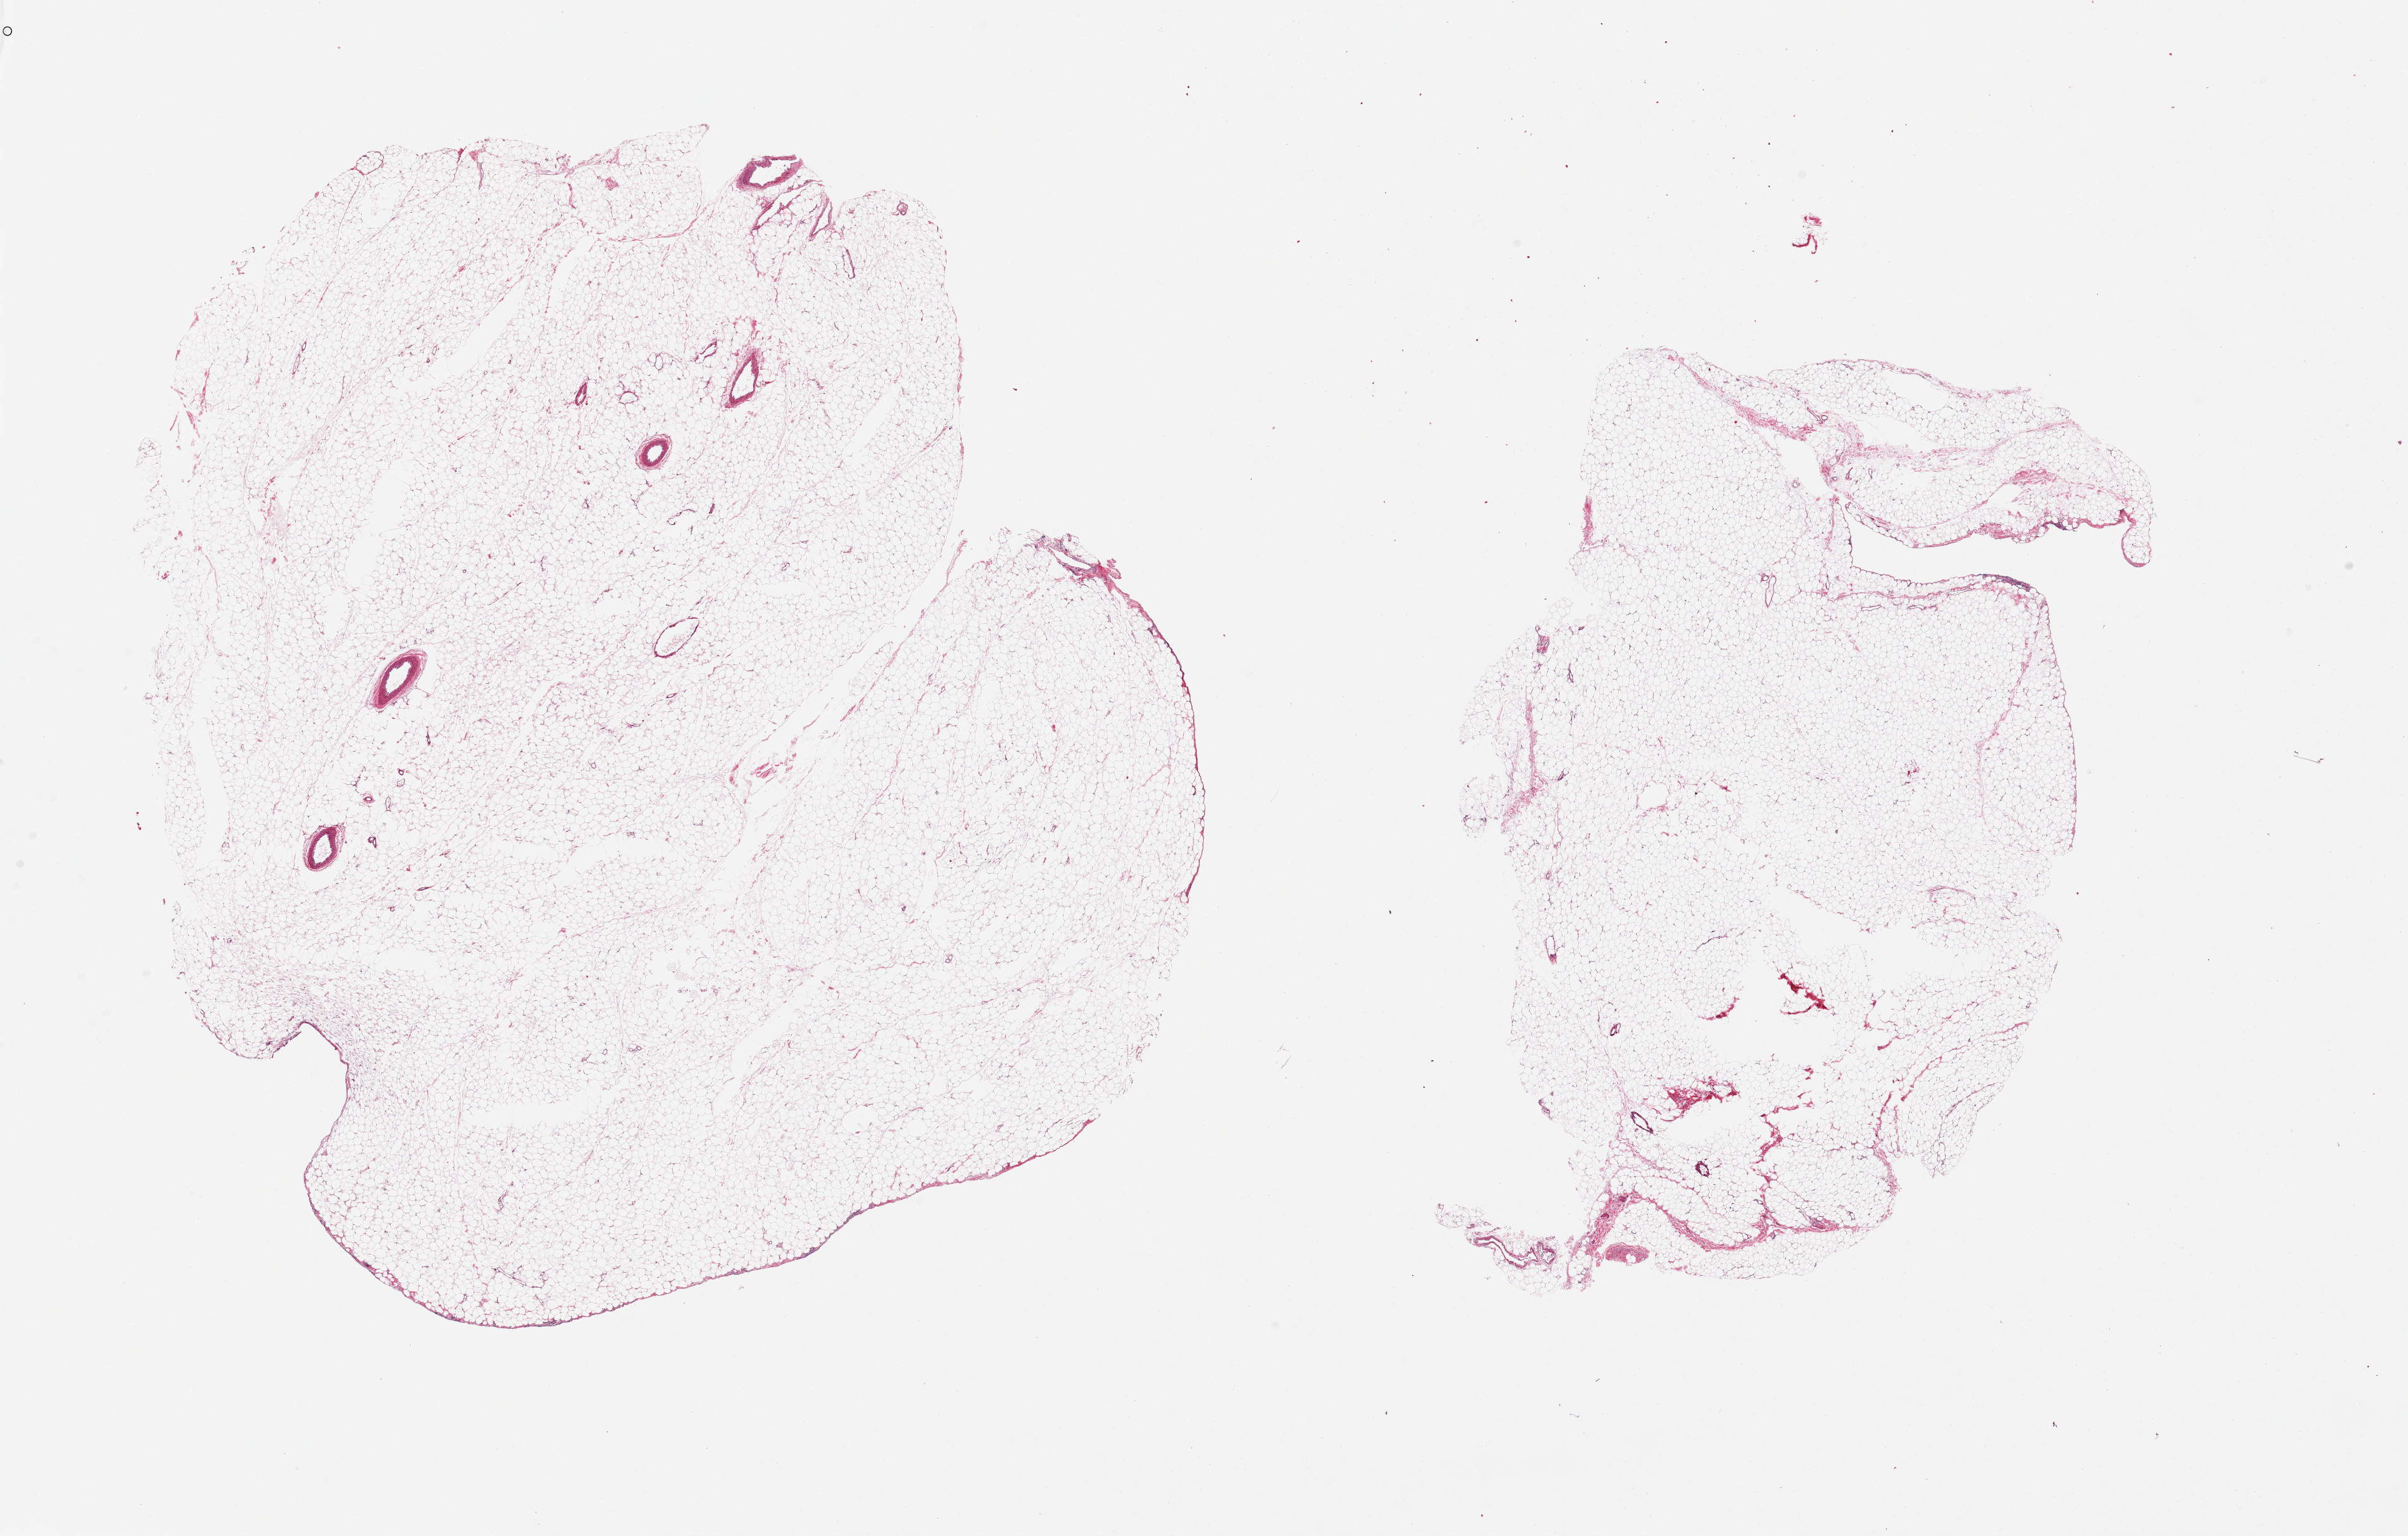
H&E whole-slide image, whole scanned area (about 30.5 x 19.5 mm, acquisition: 20x scan) shown as a low-resolution overview; PAXgene-fixed, paraffin-embedded tissue; section of omentum (target tissue); donor tissue sample.
Reviewer comment on this tissue sample: 2 pieces, small central cavity in smaller piece, good specimens with only scant fibrous tissue and rare larger vessels.